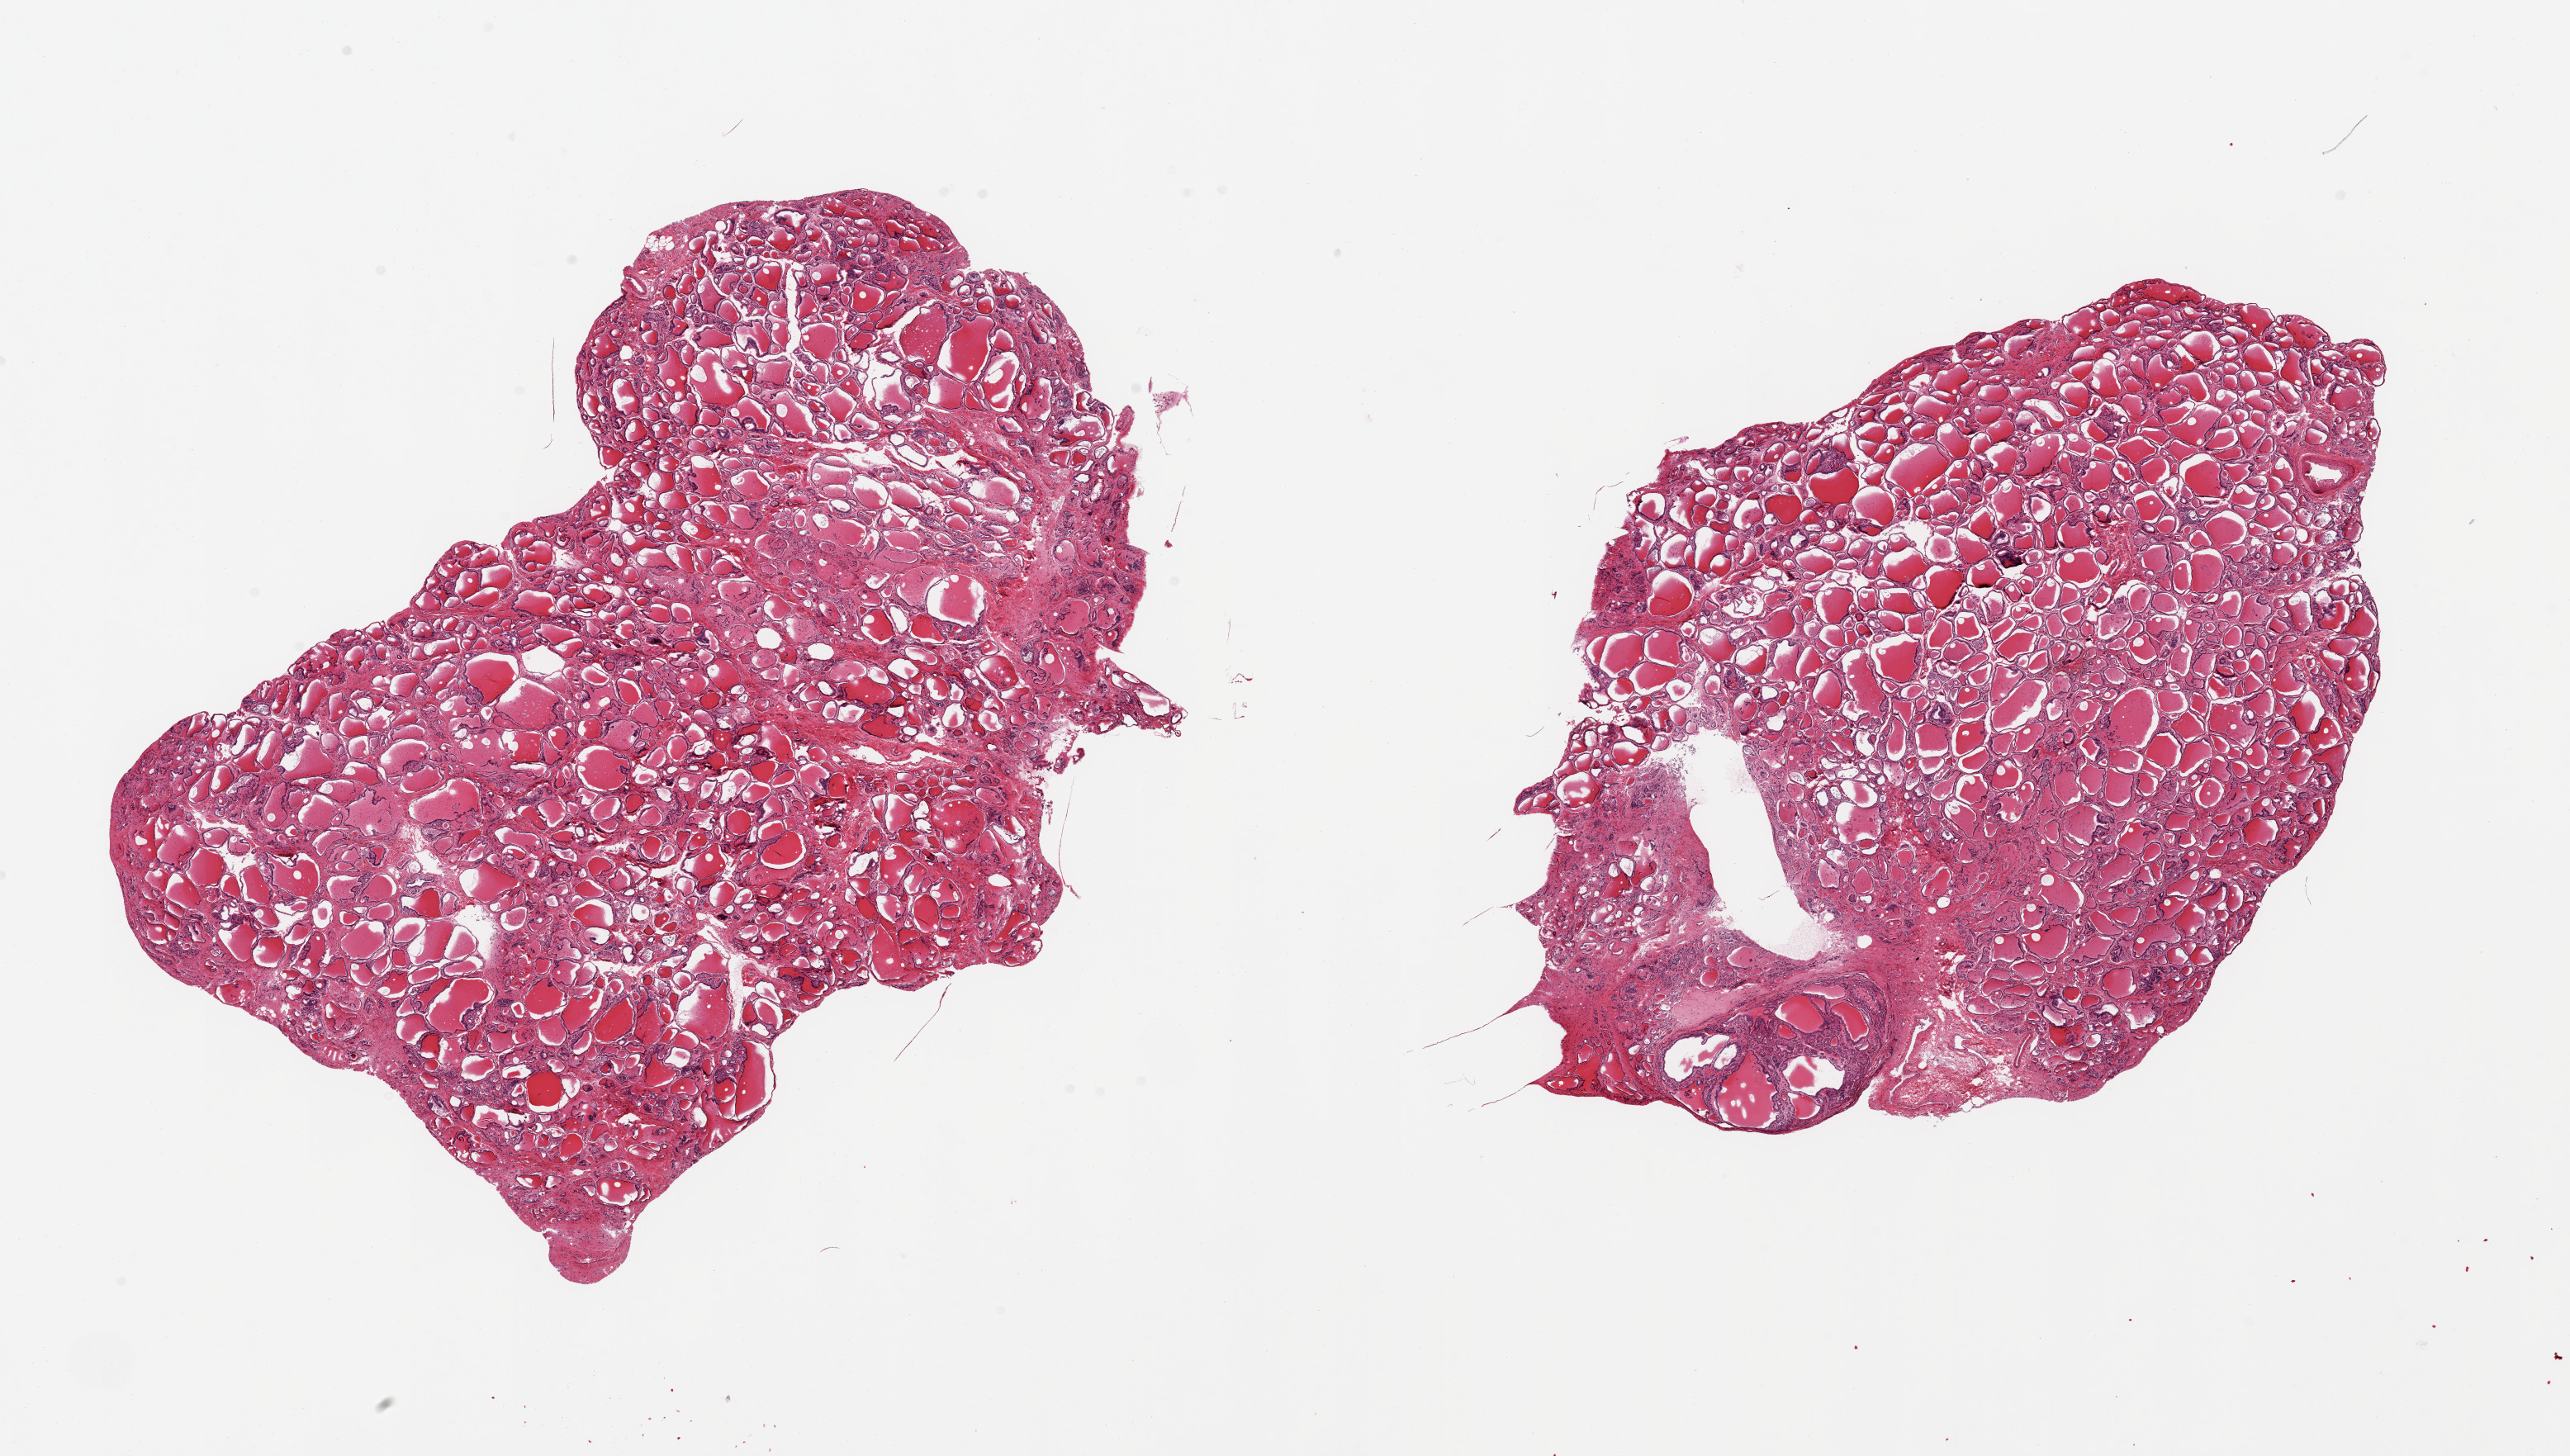
Whole-slide image, hematoxylin and eosin (H&E) stain, whole scanned area (about 24.6 x 13.9 mm) shown as a low-resolution overview, PAXgene-fixed paraffin-embedded (PFPE) section, sampled site (target tissue): thyroid, donor tissue sample. Donor sex: male.
Reviewer comment on this tissue sample: 2 pieces.